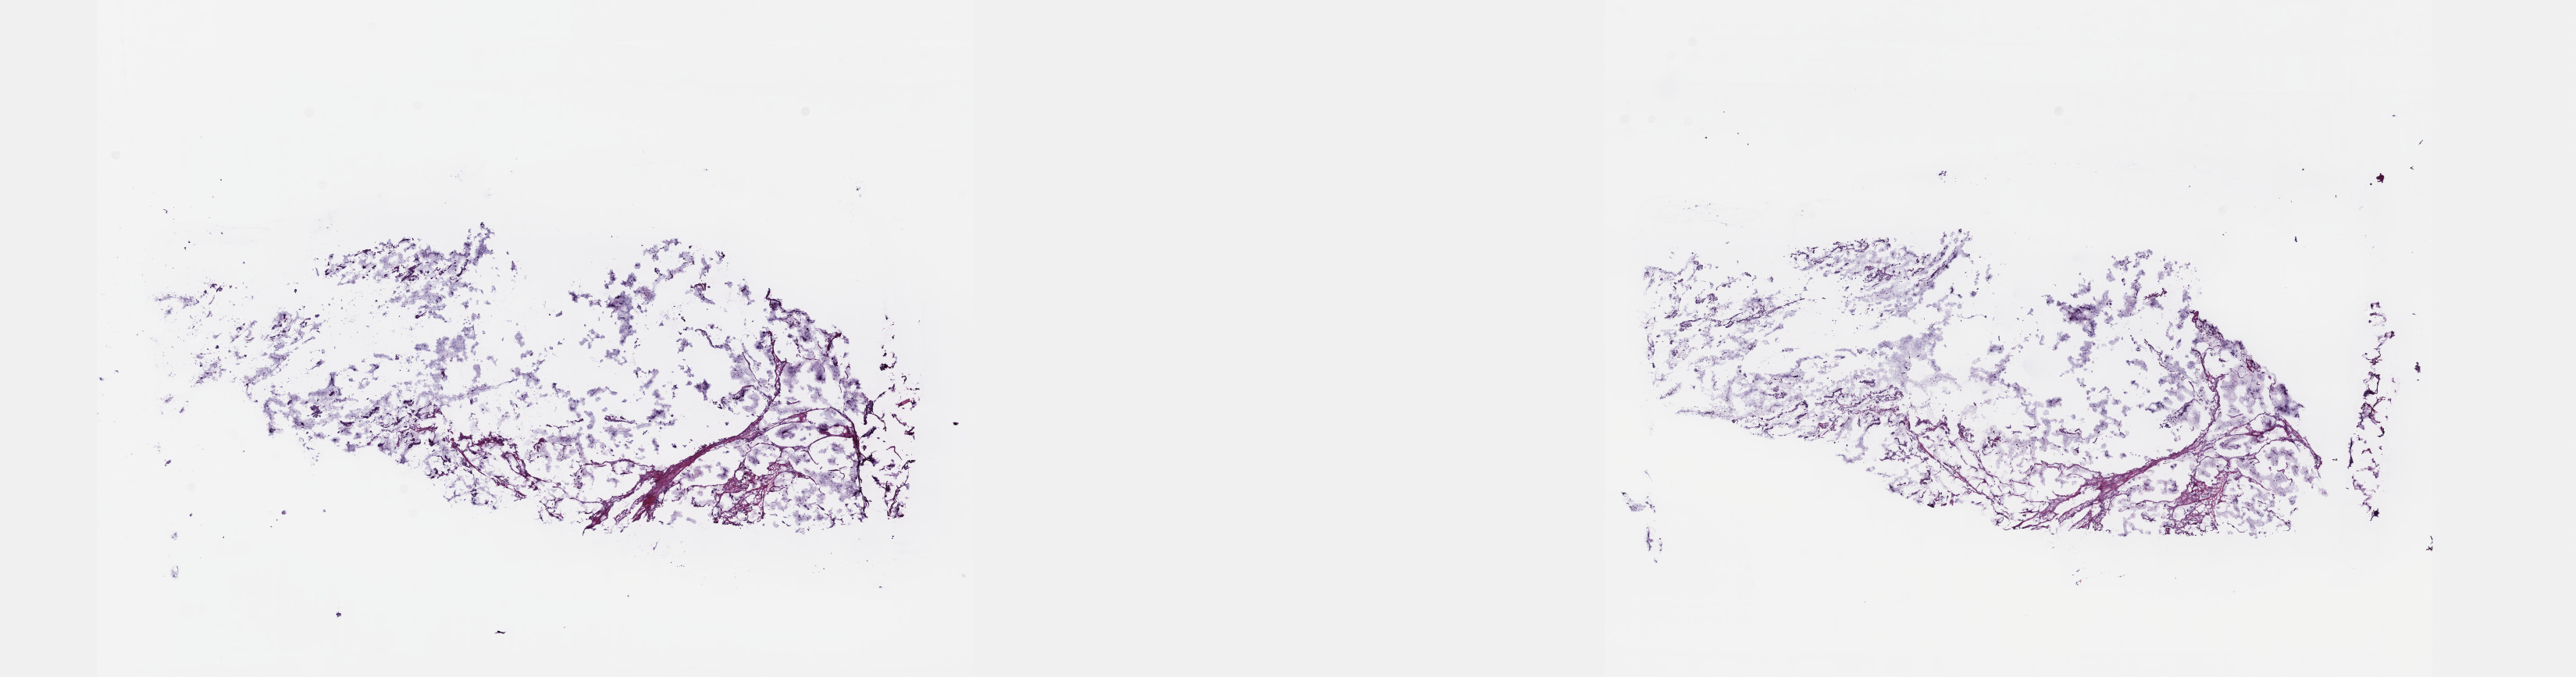
Hematoxylin and eosin (H&E) stained whole-slide image — shown as a low-resolution overview of the whole scanned area (about 26.7 x 7.0 mm). Frozen section. Stomach, primary tumour sample. Patient: male, age at initial diagnosis 78 years. Histologic grade: G2 (moderately differentiated). Composition of this section per pathologist review: tumour cells 100%, tumour nuclei 60%, normal cells 0%, stromal cells 0%, necrosis 0%. Inflammatory infiltration, as recorded: lymphocyte infiltration 2%, monocyte infiltration 0%, neutrophil infiltration 0%.
Pathologic diagnosis: Mucinous adenocarcinoma (fundus of stomach). Lymph nodes positive (case pathology): 4 of 21 examined. AJCC pathologic stage: IIIA.